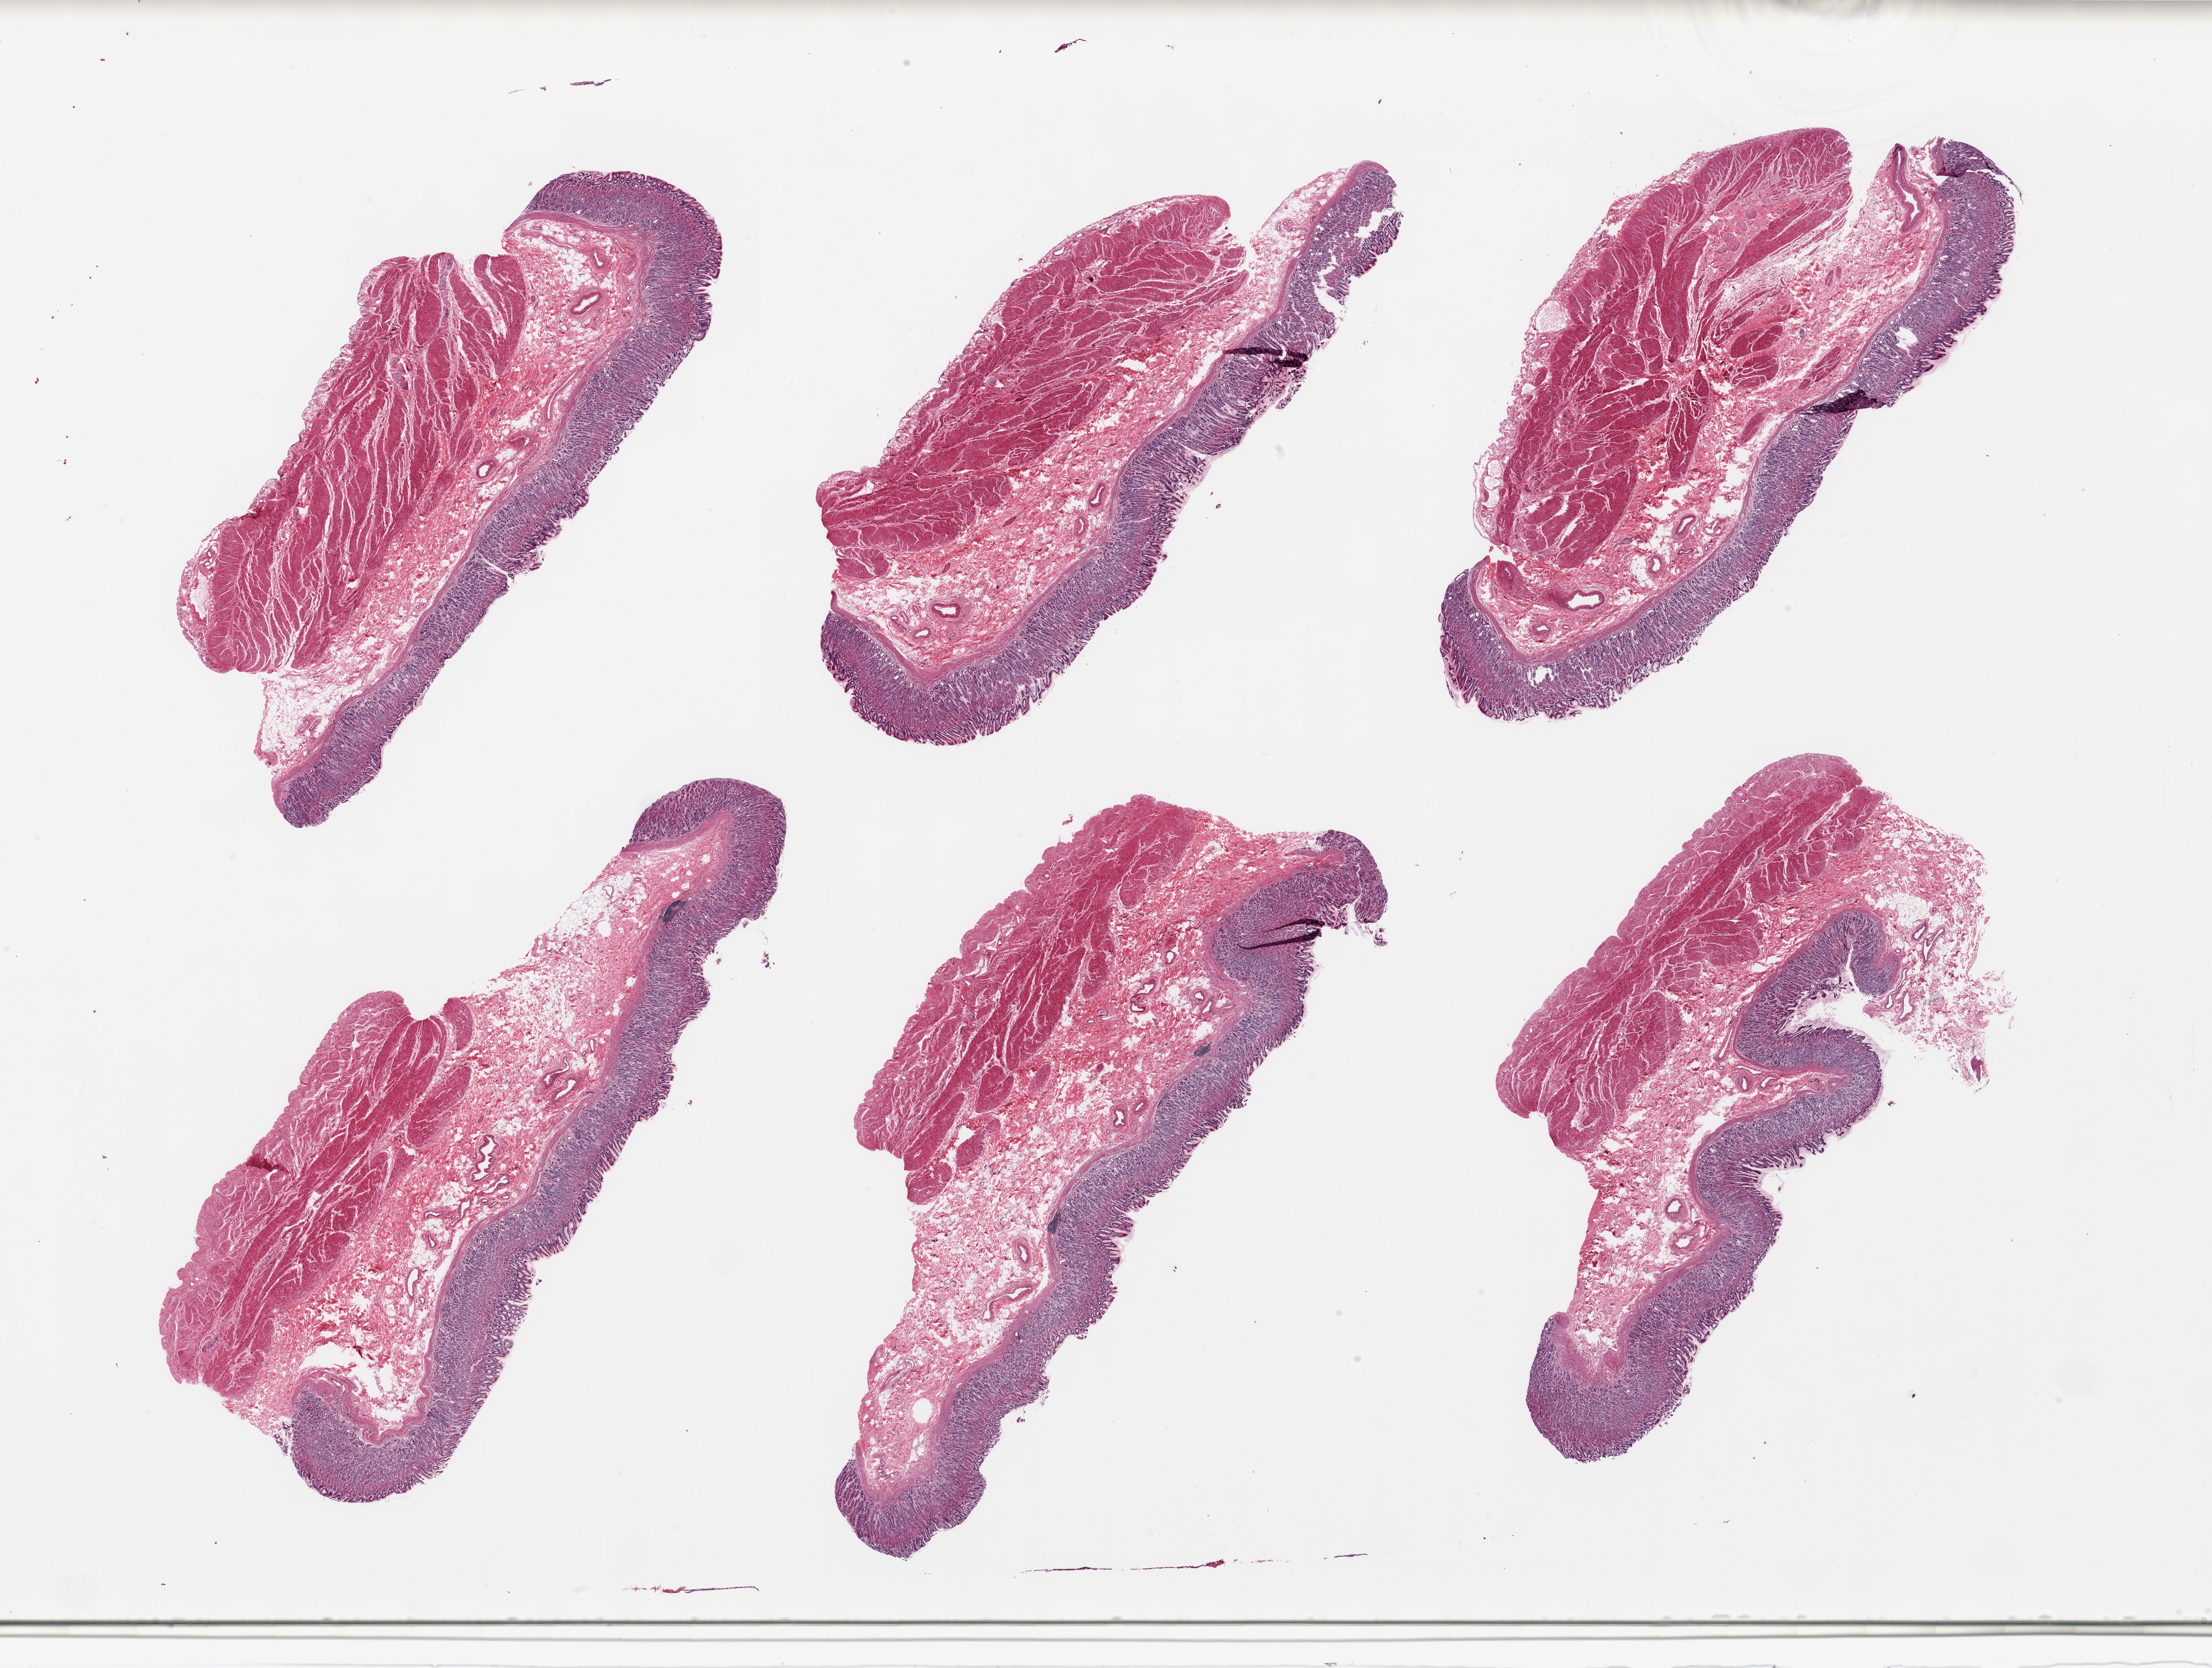
Whole-slide image, H&E stain, shown as a low-resolution overview of the whole scanned area (about 31.5 x 23.8 mm), PAXgene-fixed, paraffin-embedded tissue, sampled site (target tissue): stomach, tissue donor sample. Donor: male.
Pathologist's review note for this sample: 6 pieces, mucosa well fixed, up to ~1mm, 40-50% of thickness.